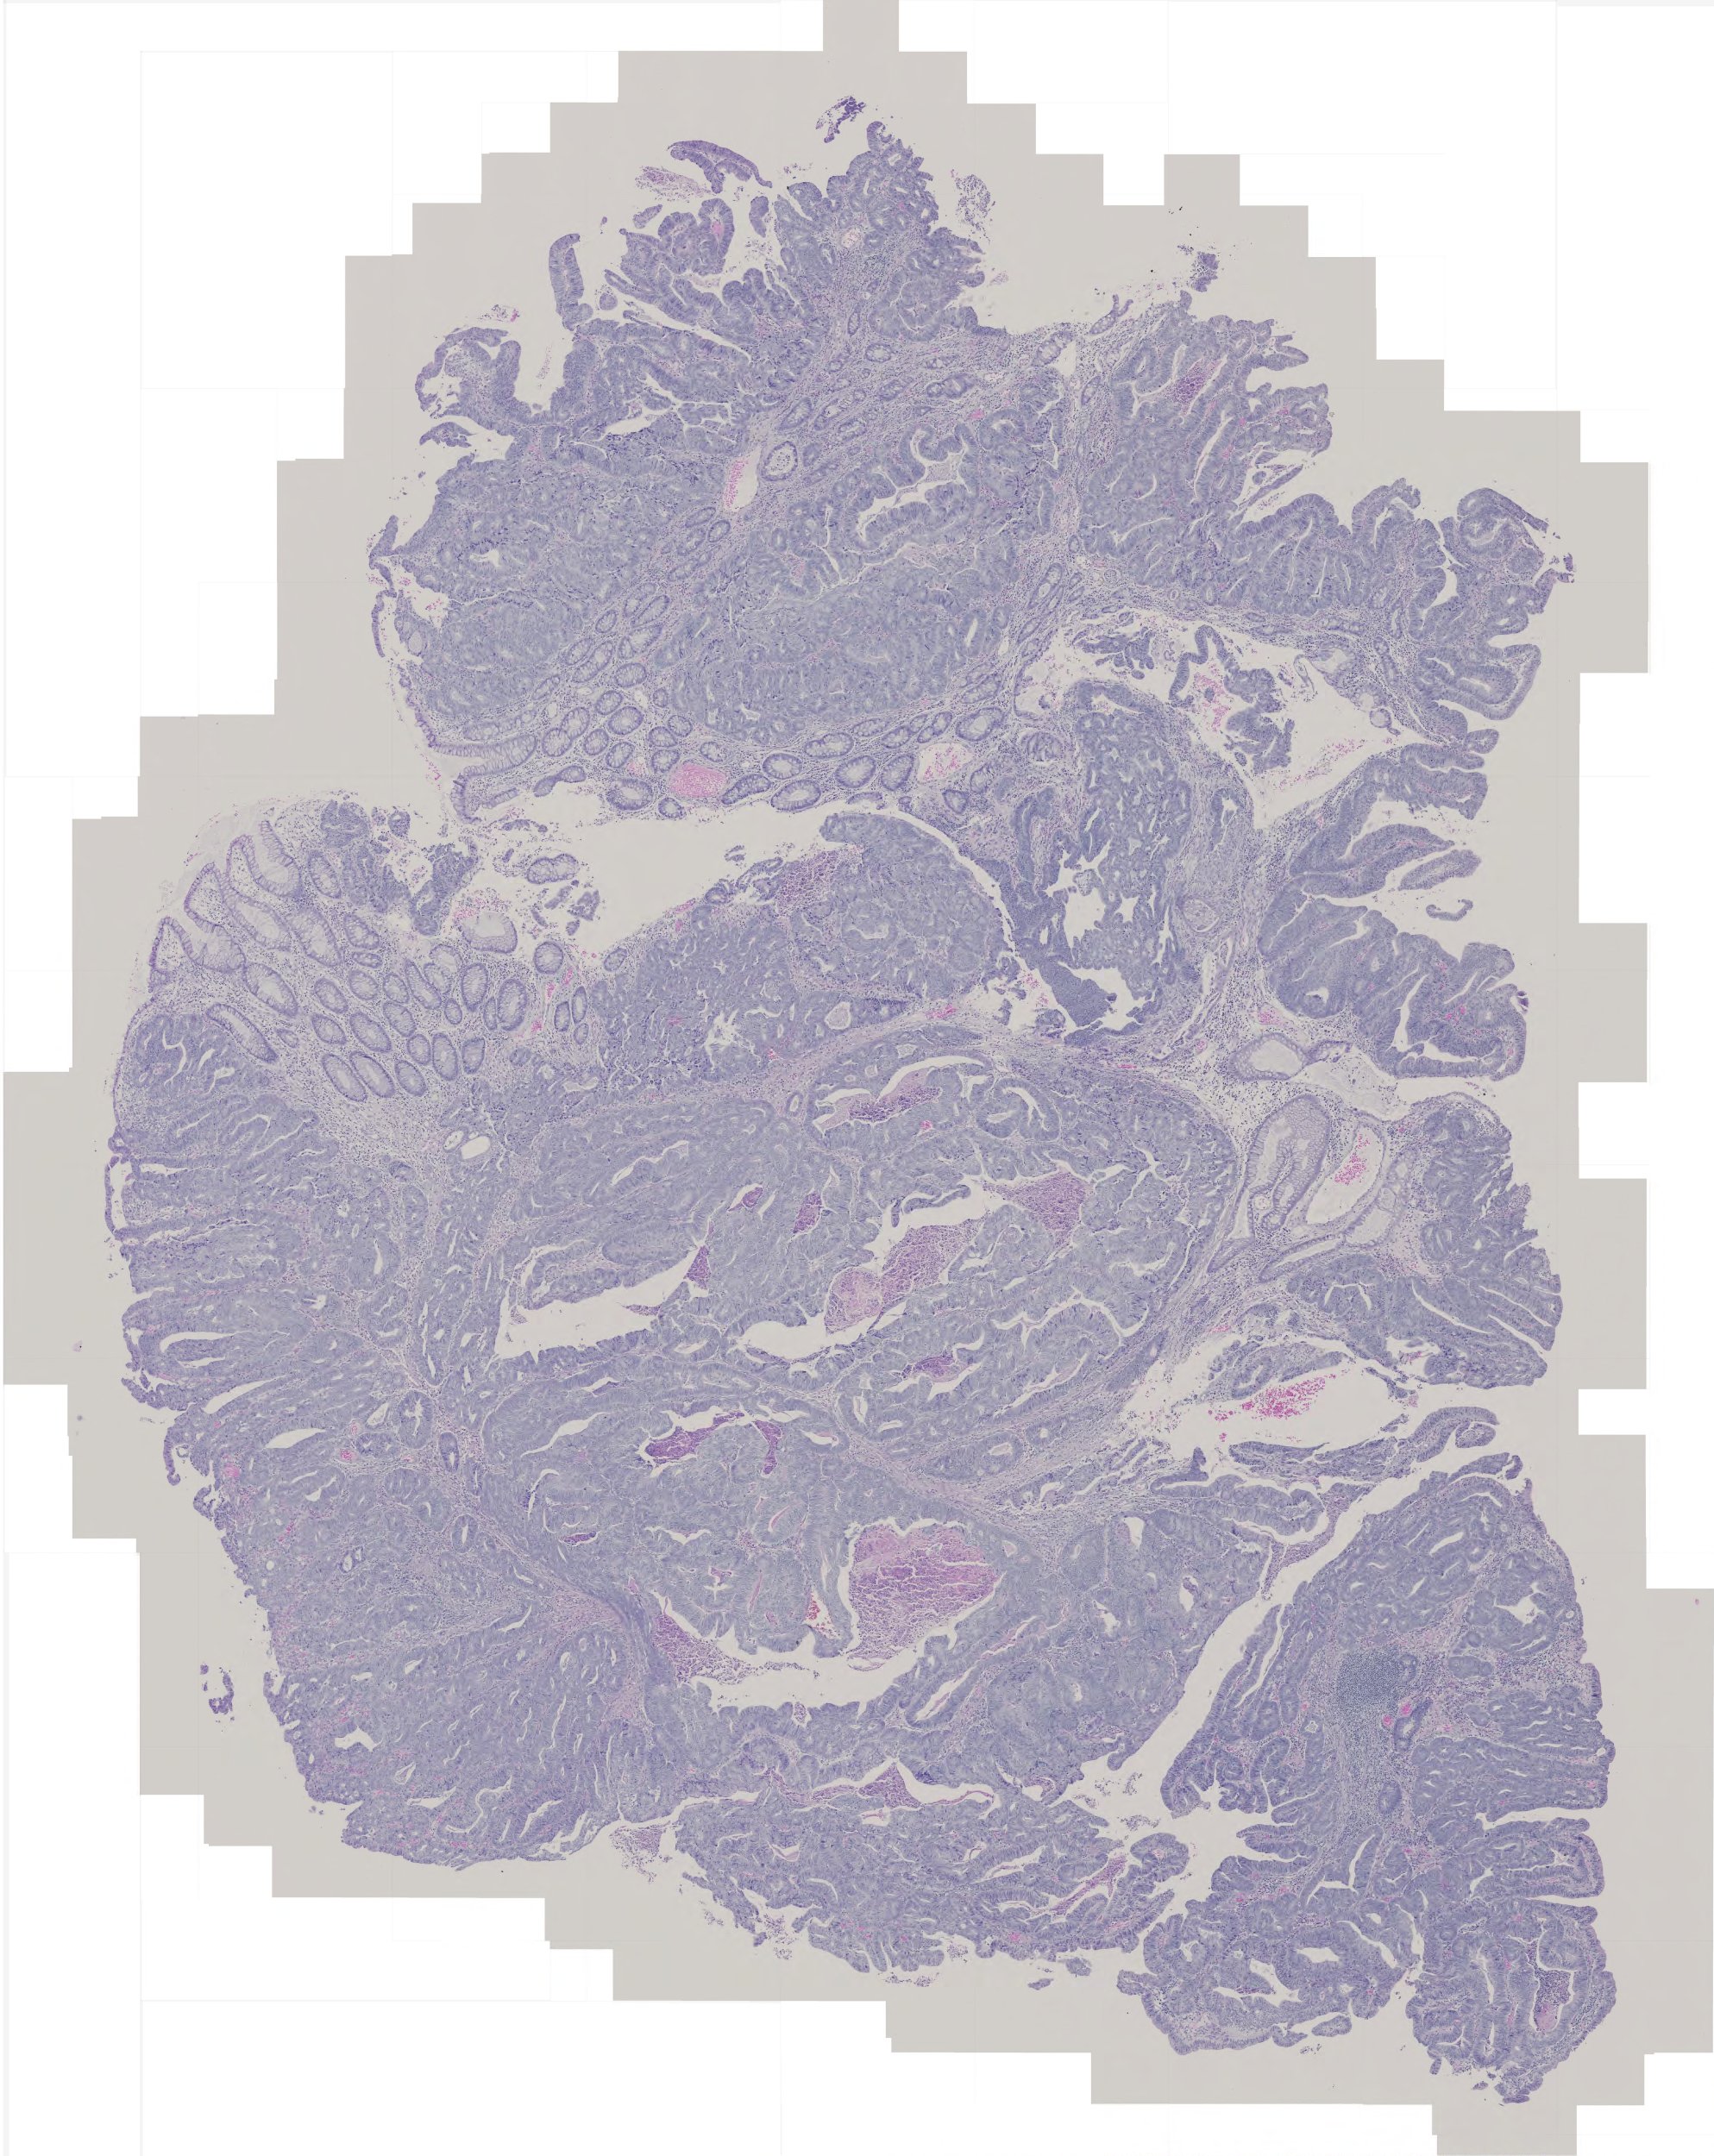
Hematoxylin and eosin (H&E) stained whole-slide image, shown as a low-resolution overview of the whole scanned area (about 4.0 x 5.0 mm). FFPE section. Colon, primary tumour sample. Patient: female, age at initial diagnosis 54 years.
Lymph nodes positive (case pathology): 0 of 27 examined. AJCC pathologic stage: II (5th edition). Histologic diagnosis: Adenocarcinoma, NOS (sigmoid colon).